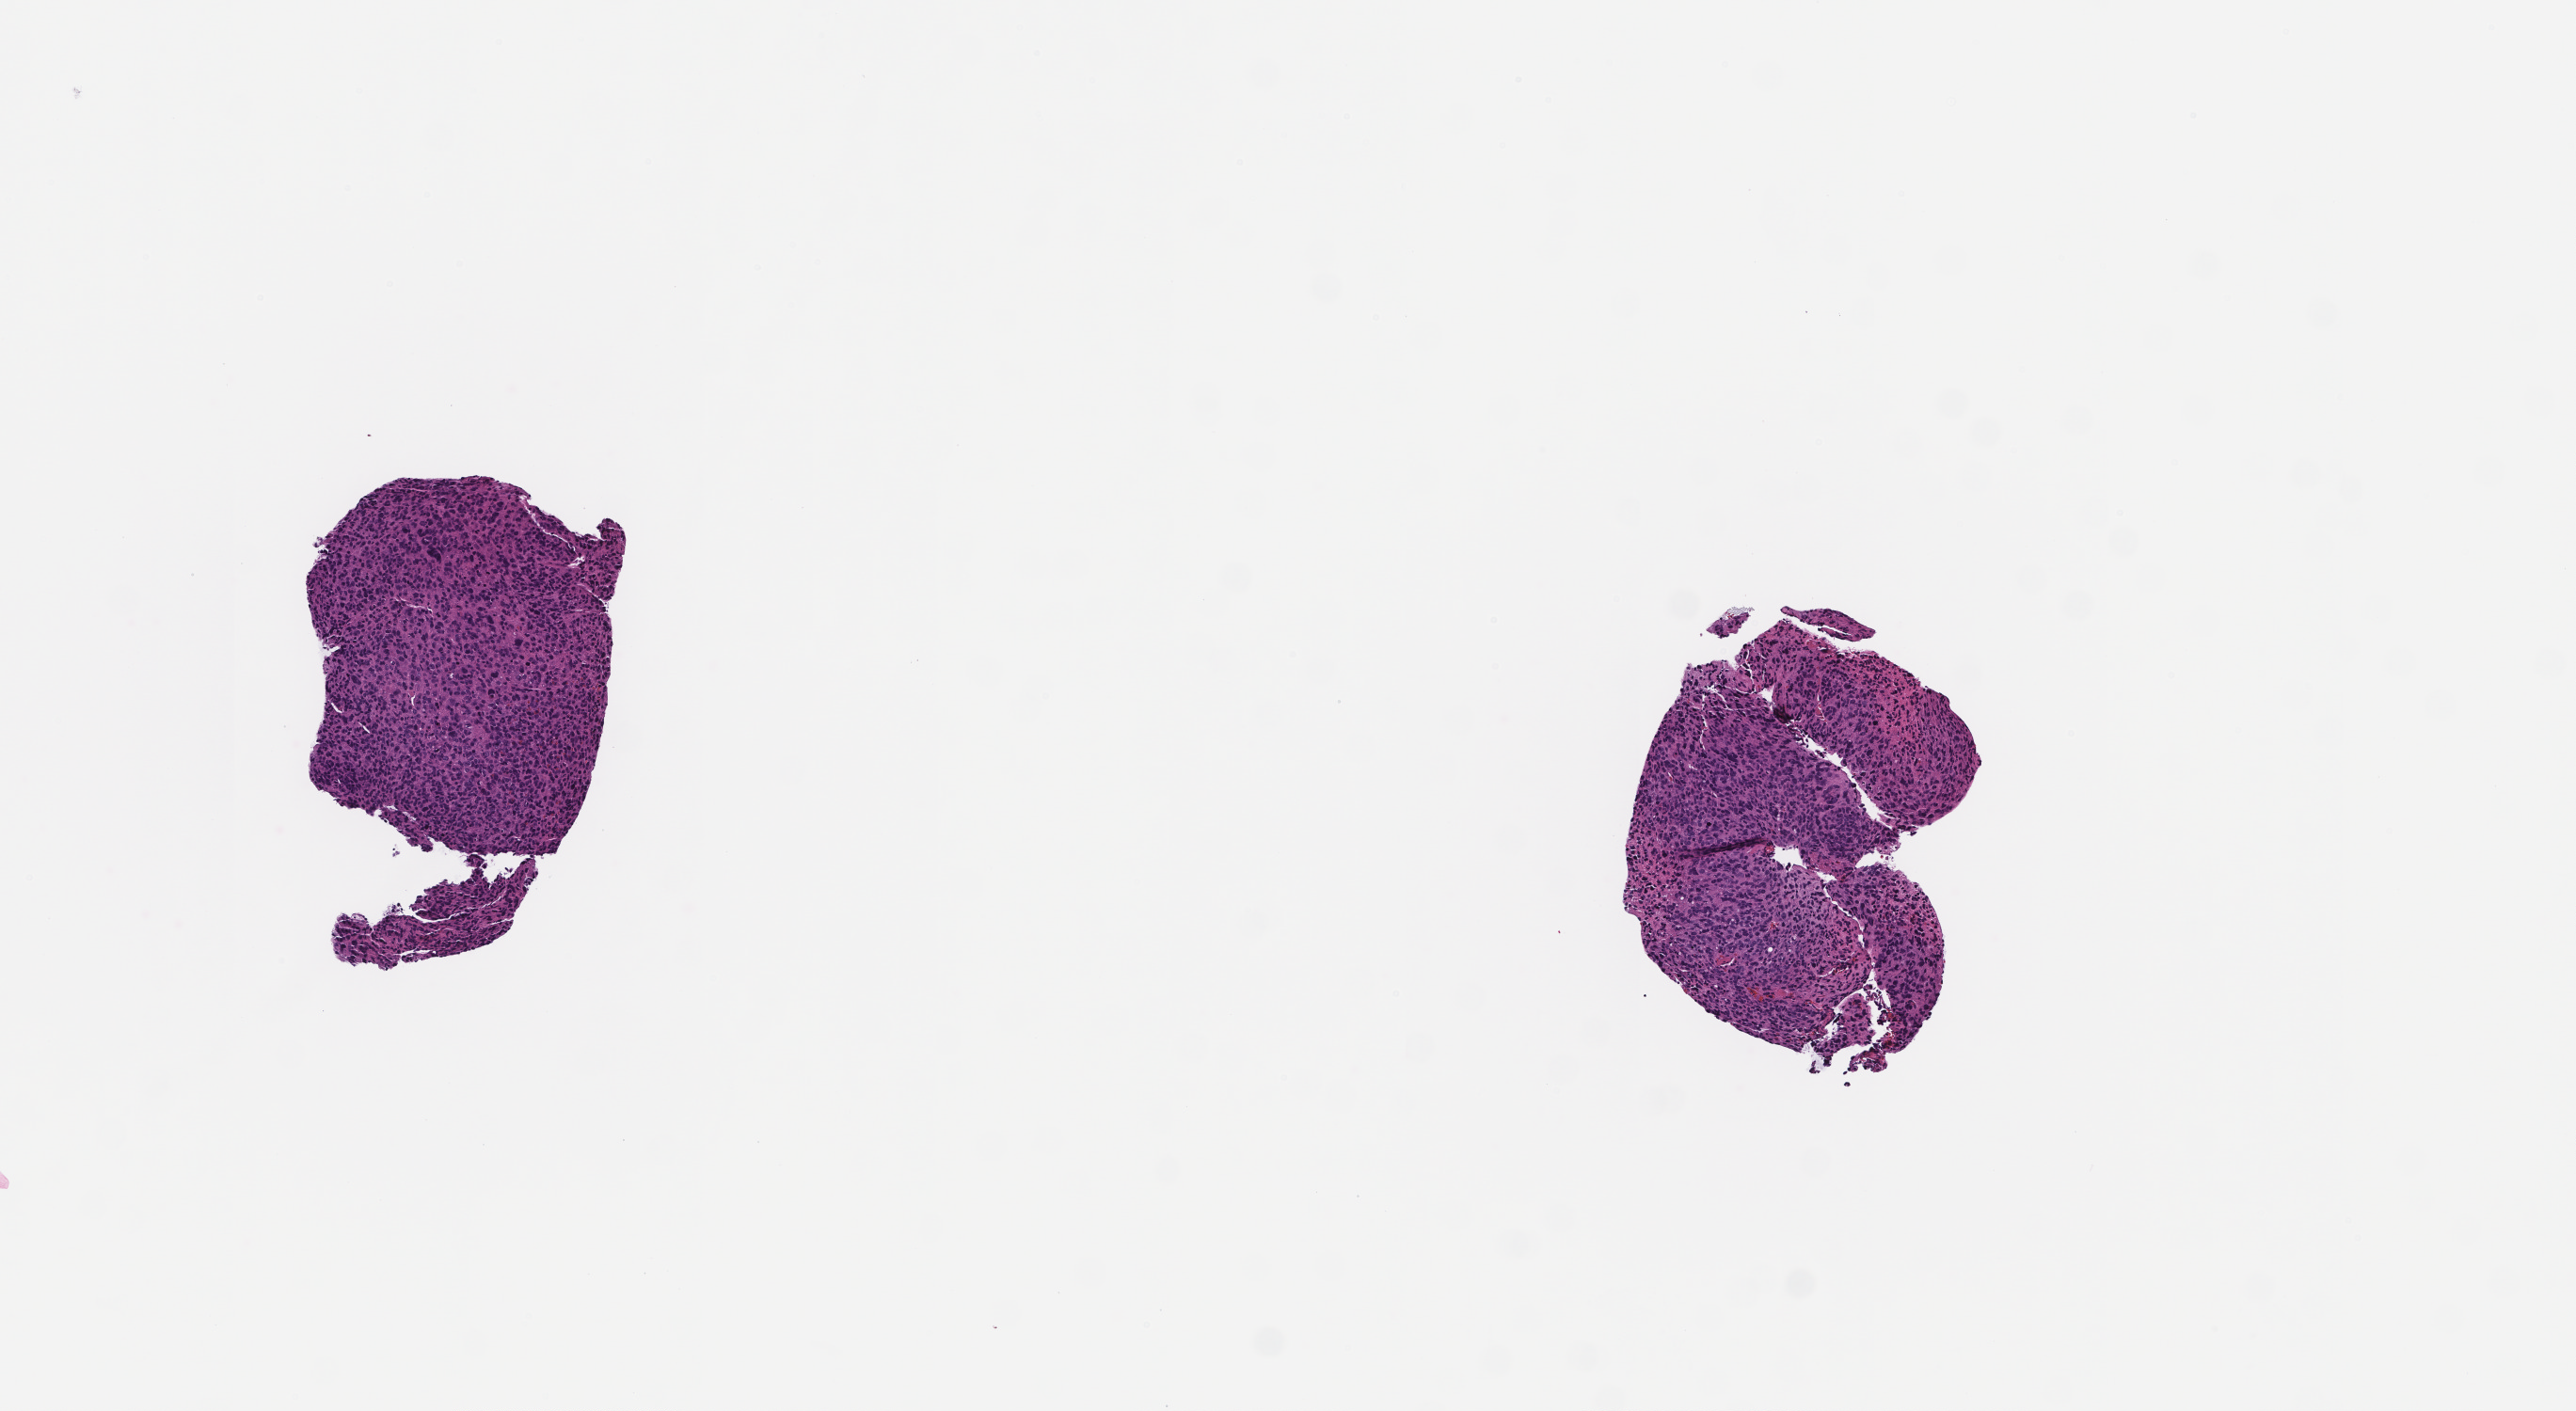
Whole-slide image, hematoxylin and eosin (H&E) stain, shown as a low-resolution overview of the whole scanned area (about 5.5 x 3.0 mm). Formalin-fixed paraffin-embedded section. Patient: female.
• this section: metastasis (sampled organ not recorded)
• patient diagnosis (primary): Invasive Breast Carcinoma